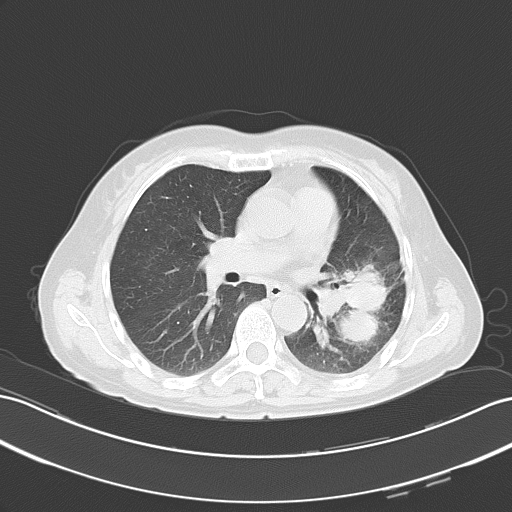
Chest CT, one axial slice; slice 28 of 51 in the series (ordered by position); reconstruction kernel B70f; lung window (W 1500 / L -600 HU); 5 mm slice thickness; 512 × 512 image matrix, field of view 353 × 353 mm. Patient: female, 54 years. From the clinical record (not read from this slice): clinical TNM (as recorded): T3 N1 M0.
Outlined on this slice (bounding box drawn by a radiologist):
- lung tumour (recorded histology: adenocarcinoma): bounding box (x1, y1, x2, y2) in pixels: (333, 266, 389, 345)